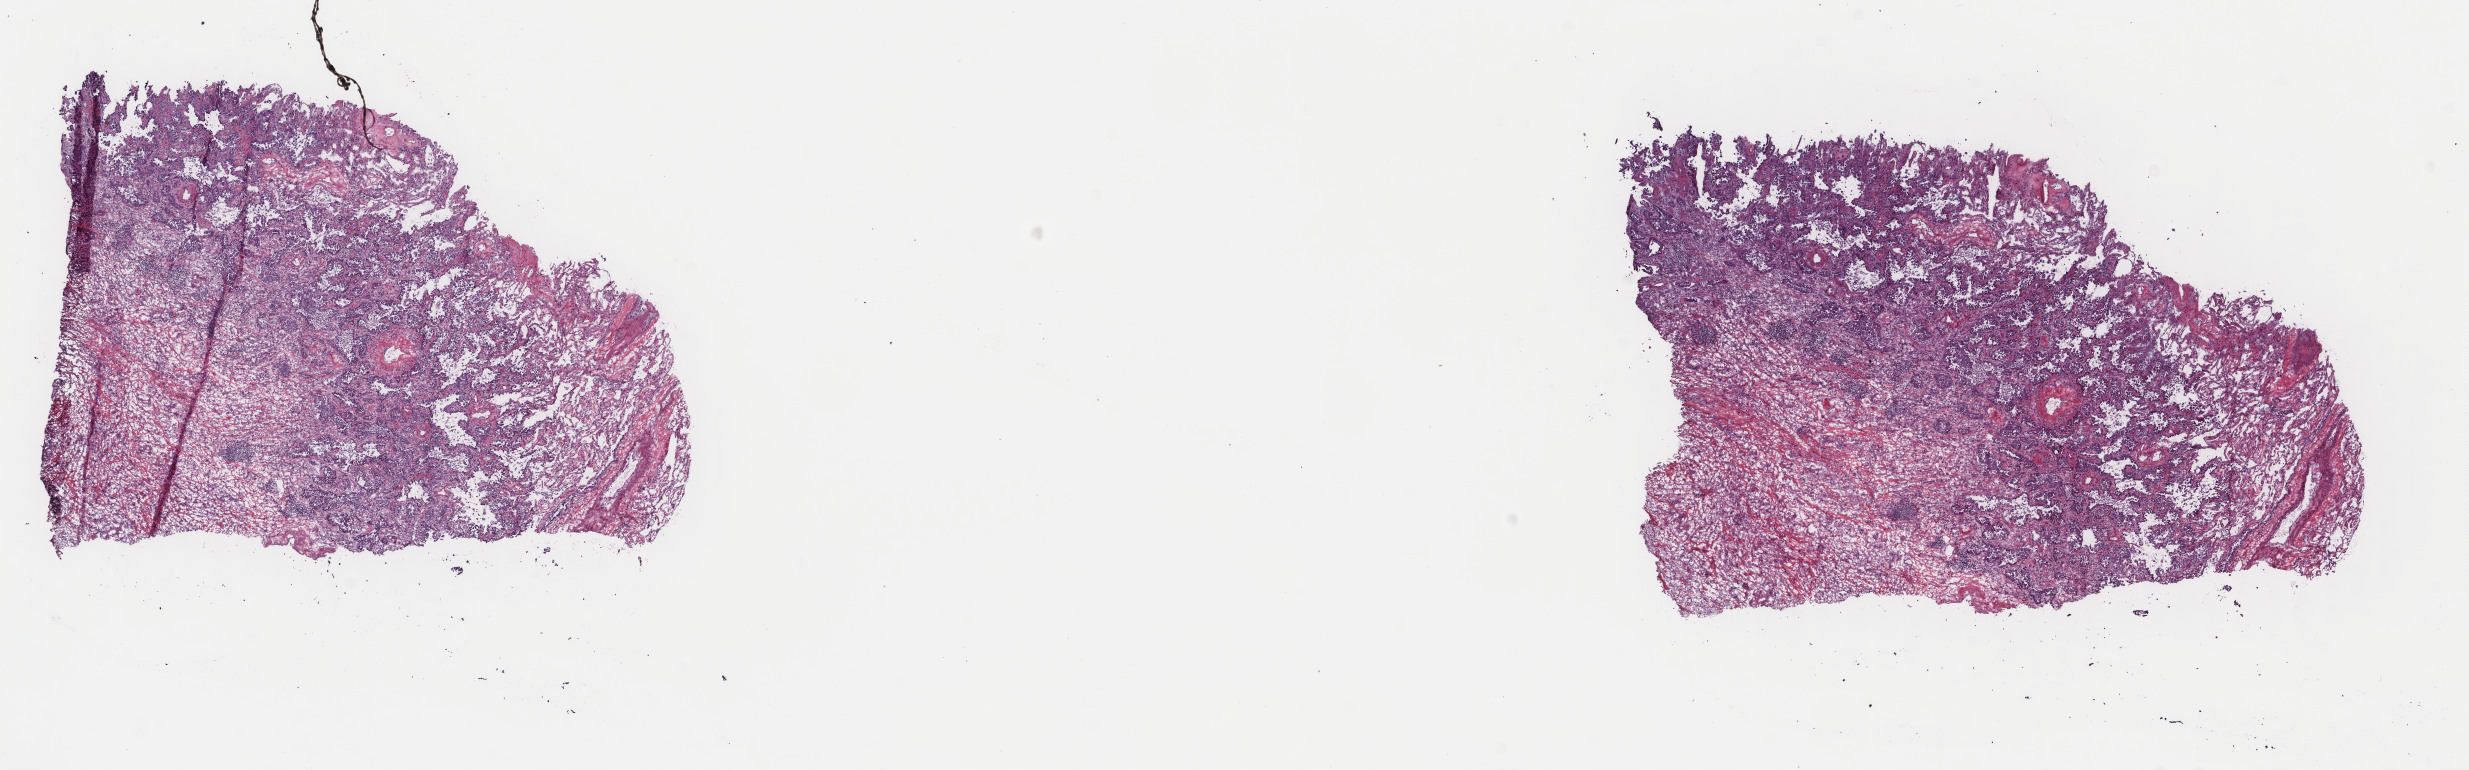
Whole-slide histology image, H&E, low-resolution overview of the scanned area, about 19.6 x 6.1 mm; frozen section from the top of the tissue portion; lung, primary tumour sample. Female patient; age at initial diagnosis 80 years. Composition of this section per pathologist review: tumour cells 50%, tumour nuclei 85%, normal cells 0%, stromal cells 50%, necrosis 0%. Infiltration values recorded for this section: lymphocyte infiltration 8%, monocyte infiltration 10%, neutrophil infiltration 0%.
- AJCC pathologic stage: IA (7th edition)
- diagnosis: Adenocarcinoma with mixed subtypes (upper lobe, lung)
- laterality: left